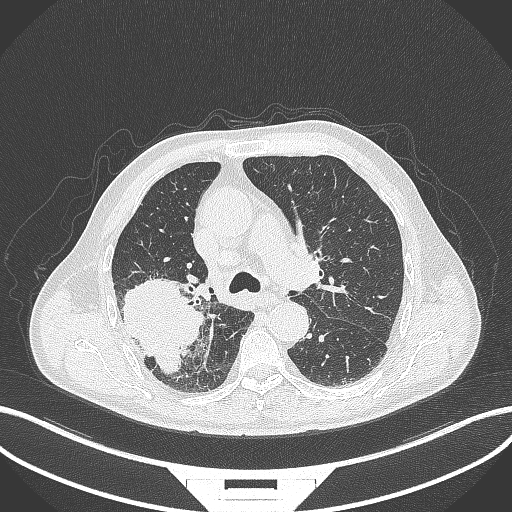
Chest CT, one axial slice; position 267 of 429 along the scan axis; 120 kVp; lung window (W 1500 / L -600 HU); 1 mm slice thickness; 512 × 512 image matrix, field of view 400 × 400 mm. Patient: male, 72 years. From the clinical record (not read from this slice): clinical TNM (as recorded): T3 N2 M0.
Outlined on this slice (rectangle marked by the reading radiologist):
- lung tumour (recorded histology: adenocarcinoma): bounding box (x1, y1, x2, y2) in pixels: (114, 275, 208, 378)